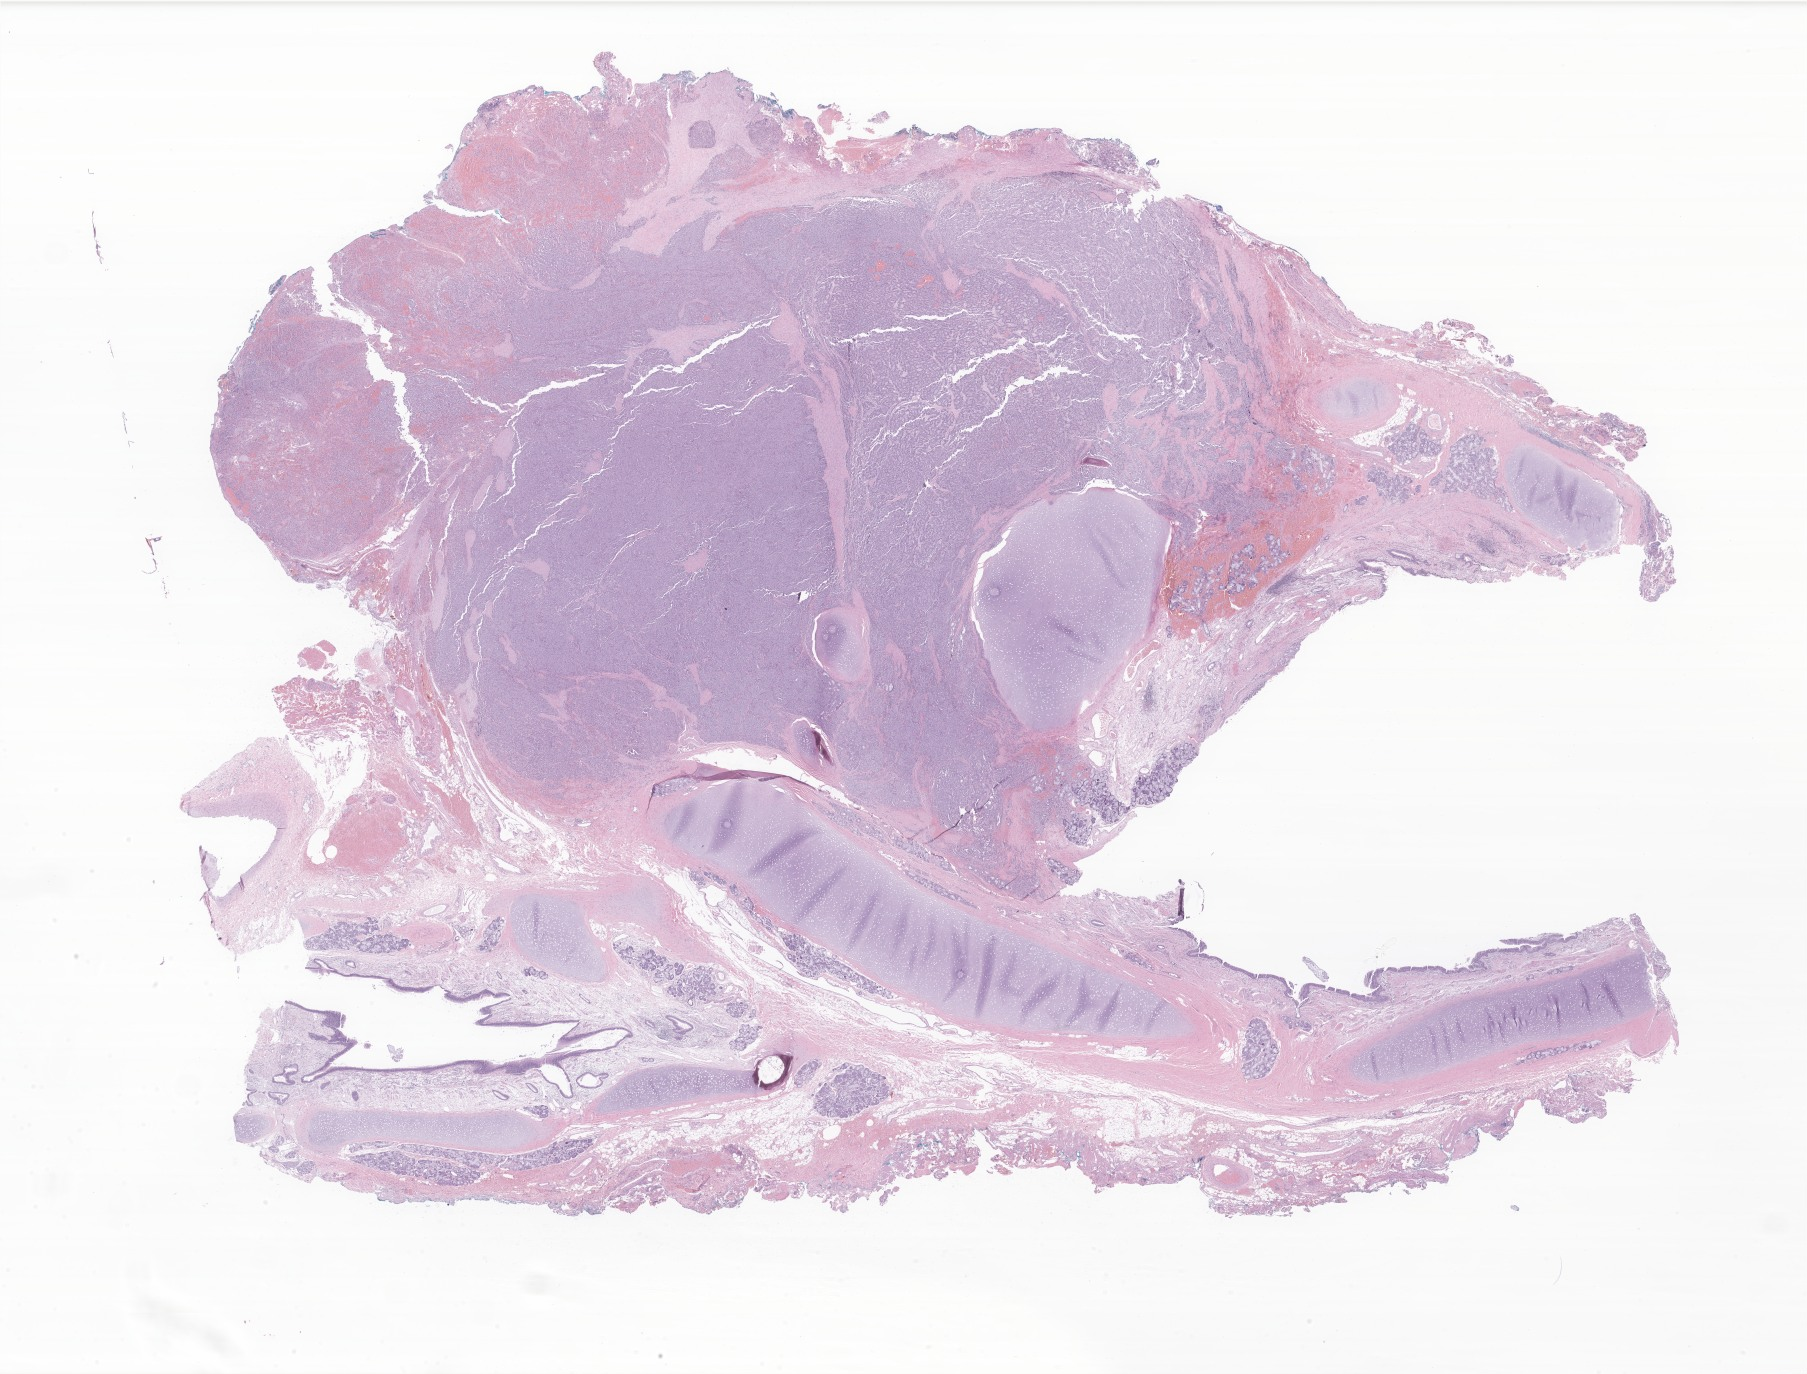
Haematoxylin and eosin whole-slide image of tumor tissue from the middle lobe of right lung — whole scanned area (about 30.5 x 23.2 mm) shown as a low-resolution overview, formalin-fixed paraffin-embedded section. Female patient, age 222 months (18 years 6 months).
Diagnosis: Neuroendocrine tumor, NOS. Tissue or organ of origin (case record): middle lobe, lung.